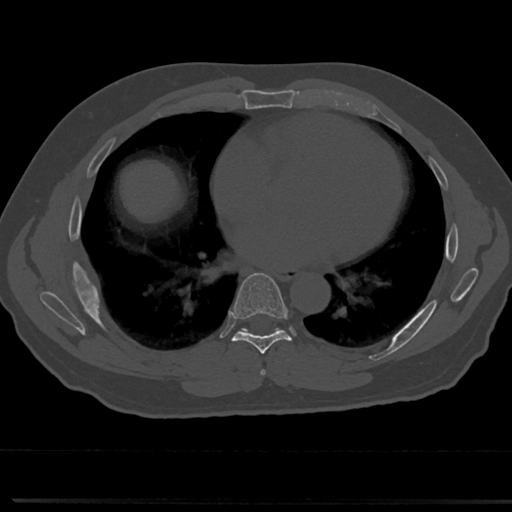
CT including the spine, one axial slice. Position 399 of 817 along the scan axis. 120 kVp. Bone window (W 1800 / L 400 HU). 0.5 mm slice thickness. 512 × 512 image matrix, field of view 355 × 355 mm. Patient: male, 61 years. From the clinical record (not read from this slice): primary cancer: prostate.
Outlined on this slice (semi-automatically segmented with operator editing):
- T6 vertebra: bounding box (x1, y1, x2, y2) in pixels: (261, 340, 319, 376)
- T7 vertebra: (214, 275, 310, 358)